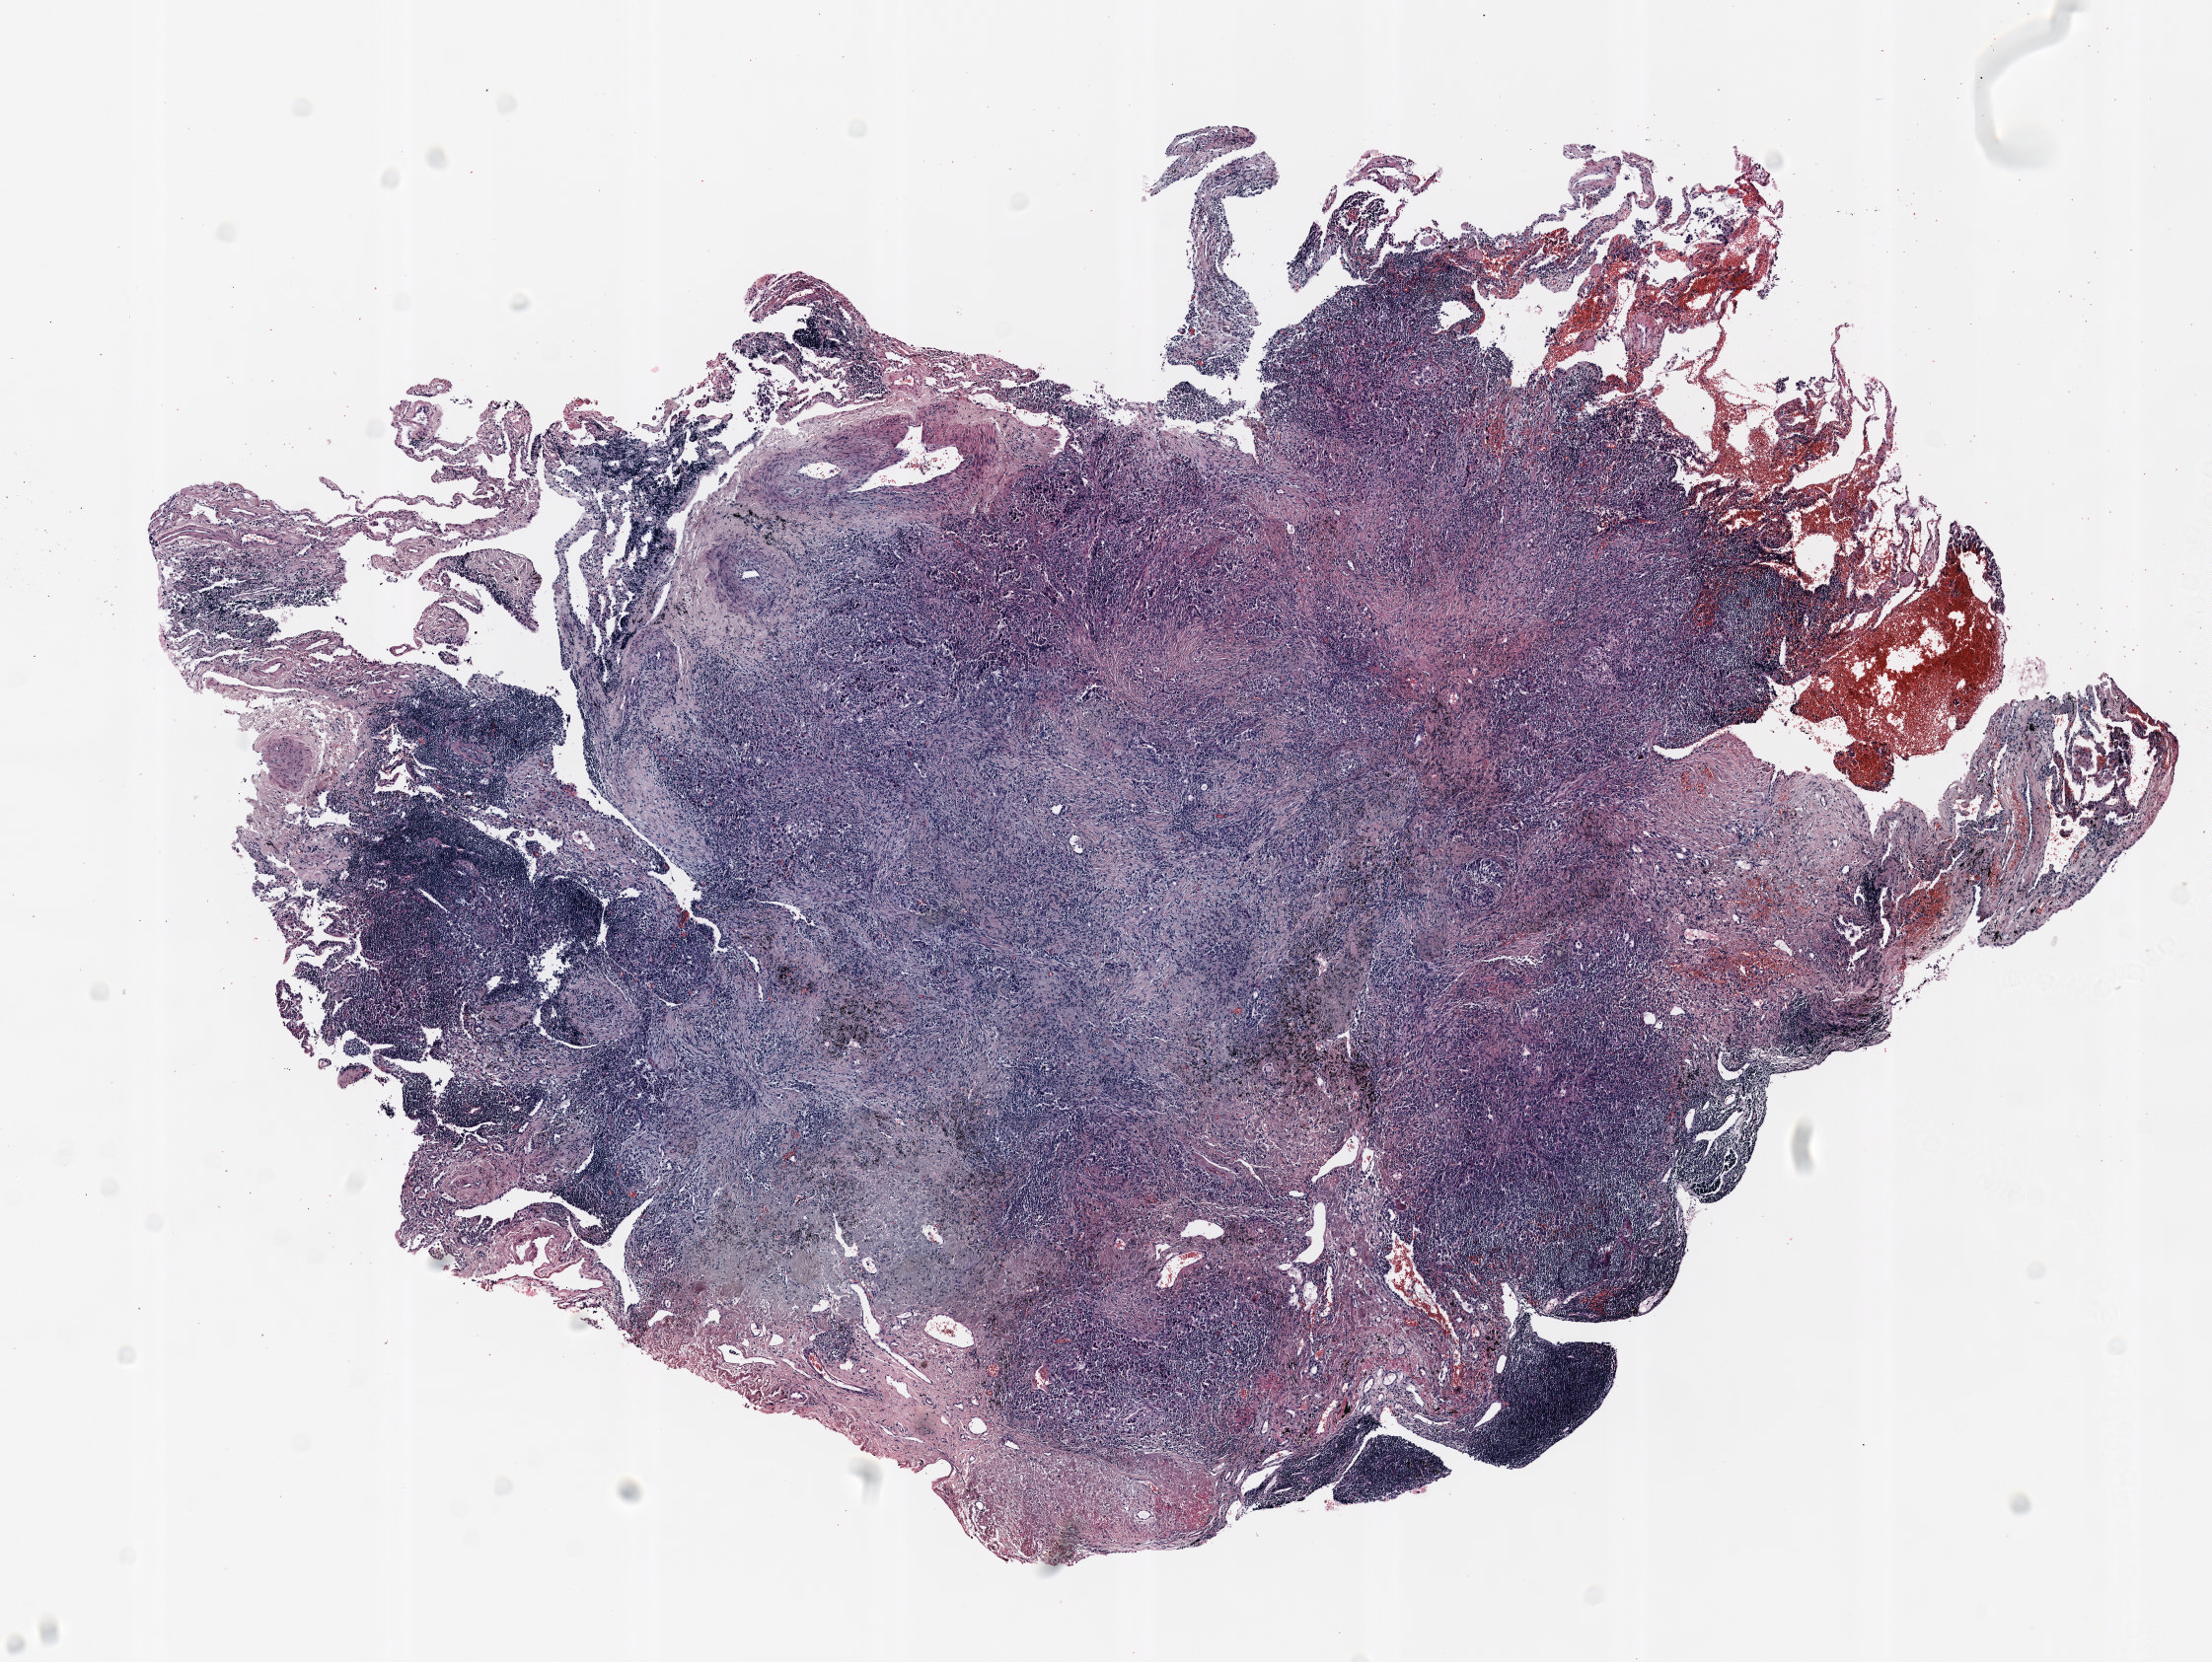
H&E-stained whole-slide image — shown as a low-resolution overview of the whole scanned area (about 9.0 x 6.8 mm, slide scanned at 20x). FFPE section. Lung tissue. Male, age 62 at enrolment. Grade: moderately differentiated (G2).
Primary tumour location (clinical record): left upper lobe. Tumour size (pathology): 10 mm. Participant's lung-cancer diagnosis: Adenocarcinoma, NOS (ICD-O-3 8140/3). Stage (AJCC 6th edition): IA. ICD-O-3 topography: upper lobe of lung (C34.1).